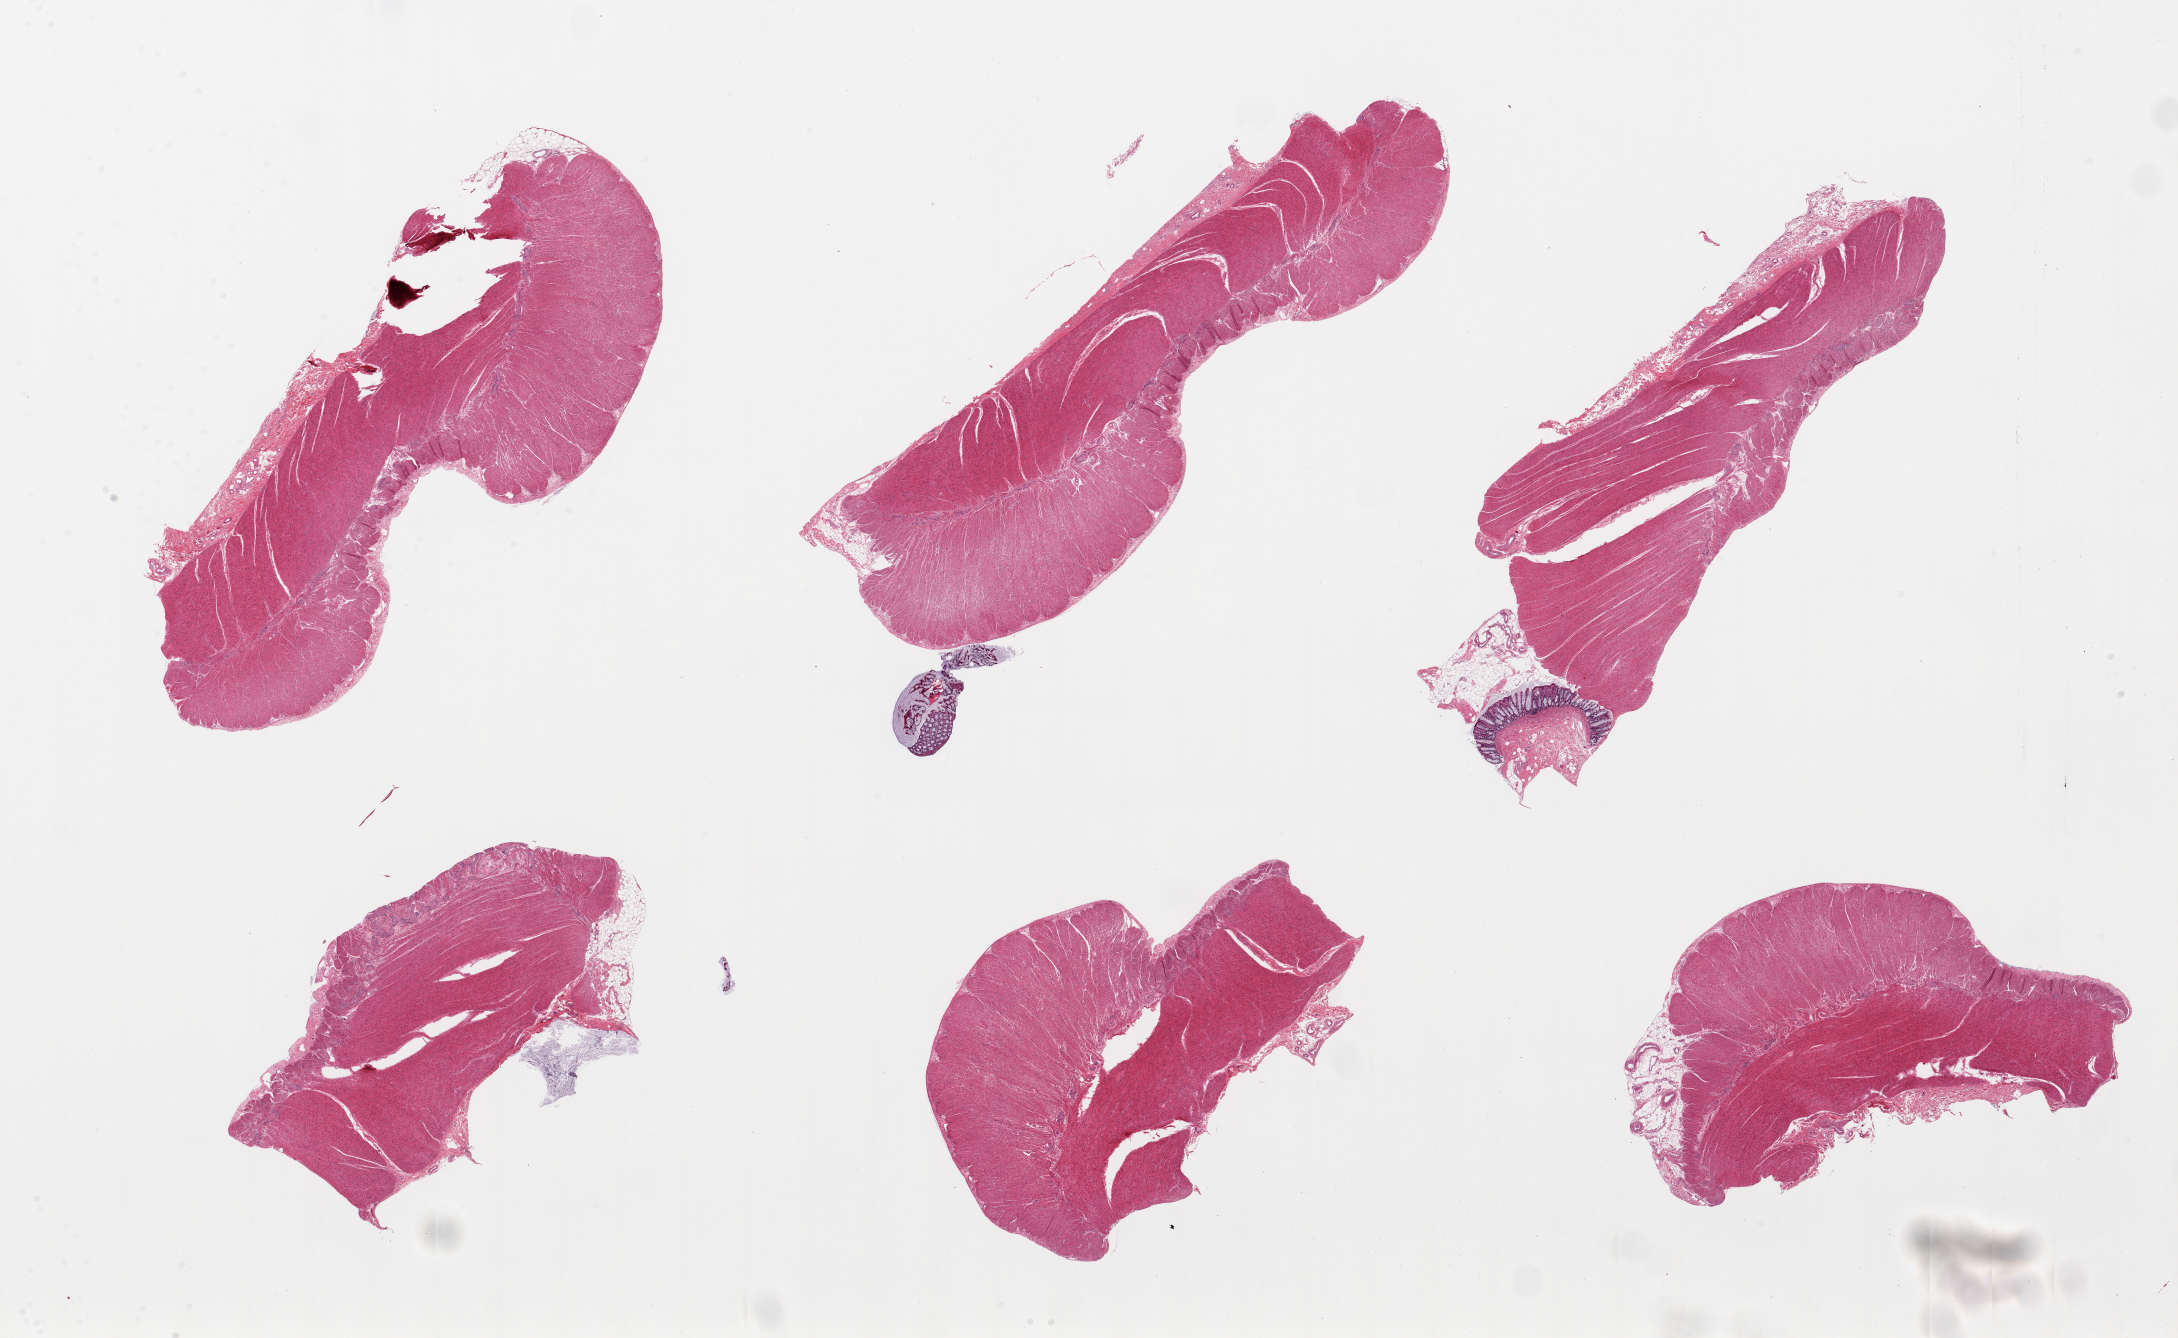
Digitized H&E-stained section, whole scanned area (about 34.5 x 21.2 mm, slide scanned at 20x) shown as a low-resolution overview; PAXgene-fixed paraffin-embedded (PFPE) section; sampled site (target tissue): sigmoid colon; donor tissue sample. Female donor.
Review note (as recorded): 6 pieces, predominantly muscularis (target) with few strips of mucosa and small amount of attached fat (not target).